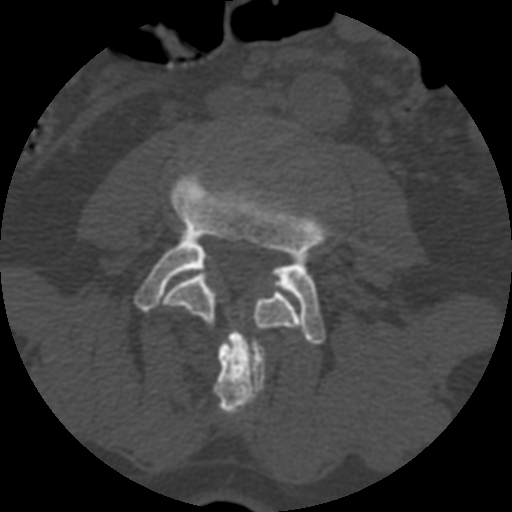
CT including the spine, one axial slice. Position 292 of 399 along the scan axis. Reconstruction kernel STANDARD. 120 kVp. Bone window (W 1800 / L 400 HU). 1.25 mm slice thickness. 512 × 512 image matrix, field of view 160 × 160 mm. Patient age 71 years. Case-level facts recorded for this patient, not image findings: primary cancer: prostate.
Annotated regions visible in this slice (semi-automatically segmented with operator editing):
- L3 vertebra: bounding box [x1, y1, x2, y2] px = [162, 271, 302, 414]
- L4 vertebra: [135, 166, 331, 344]